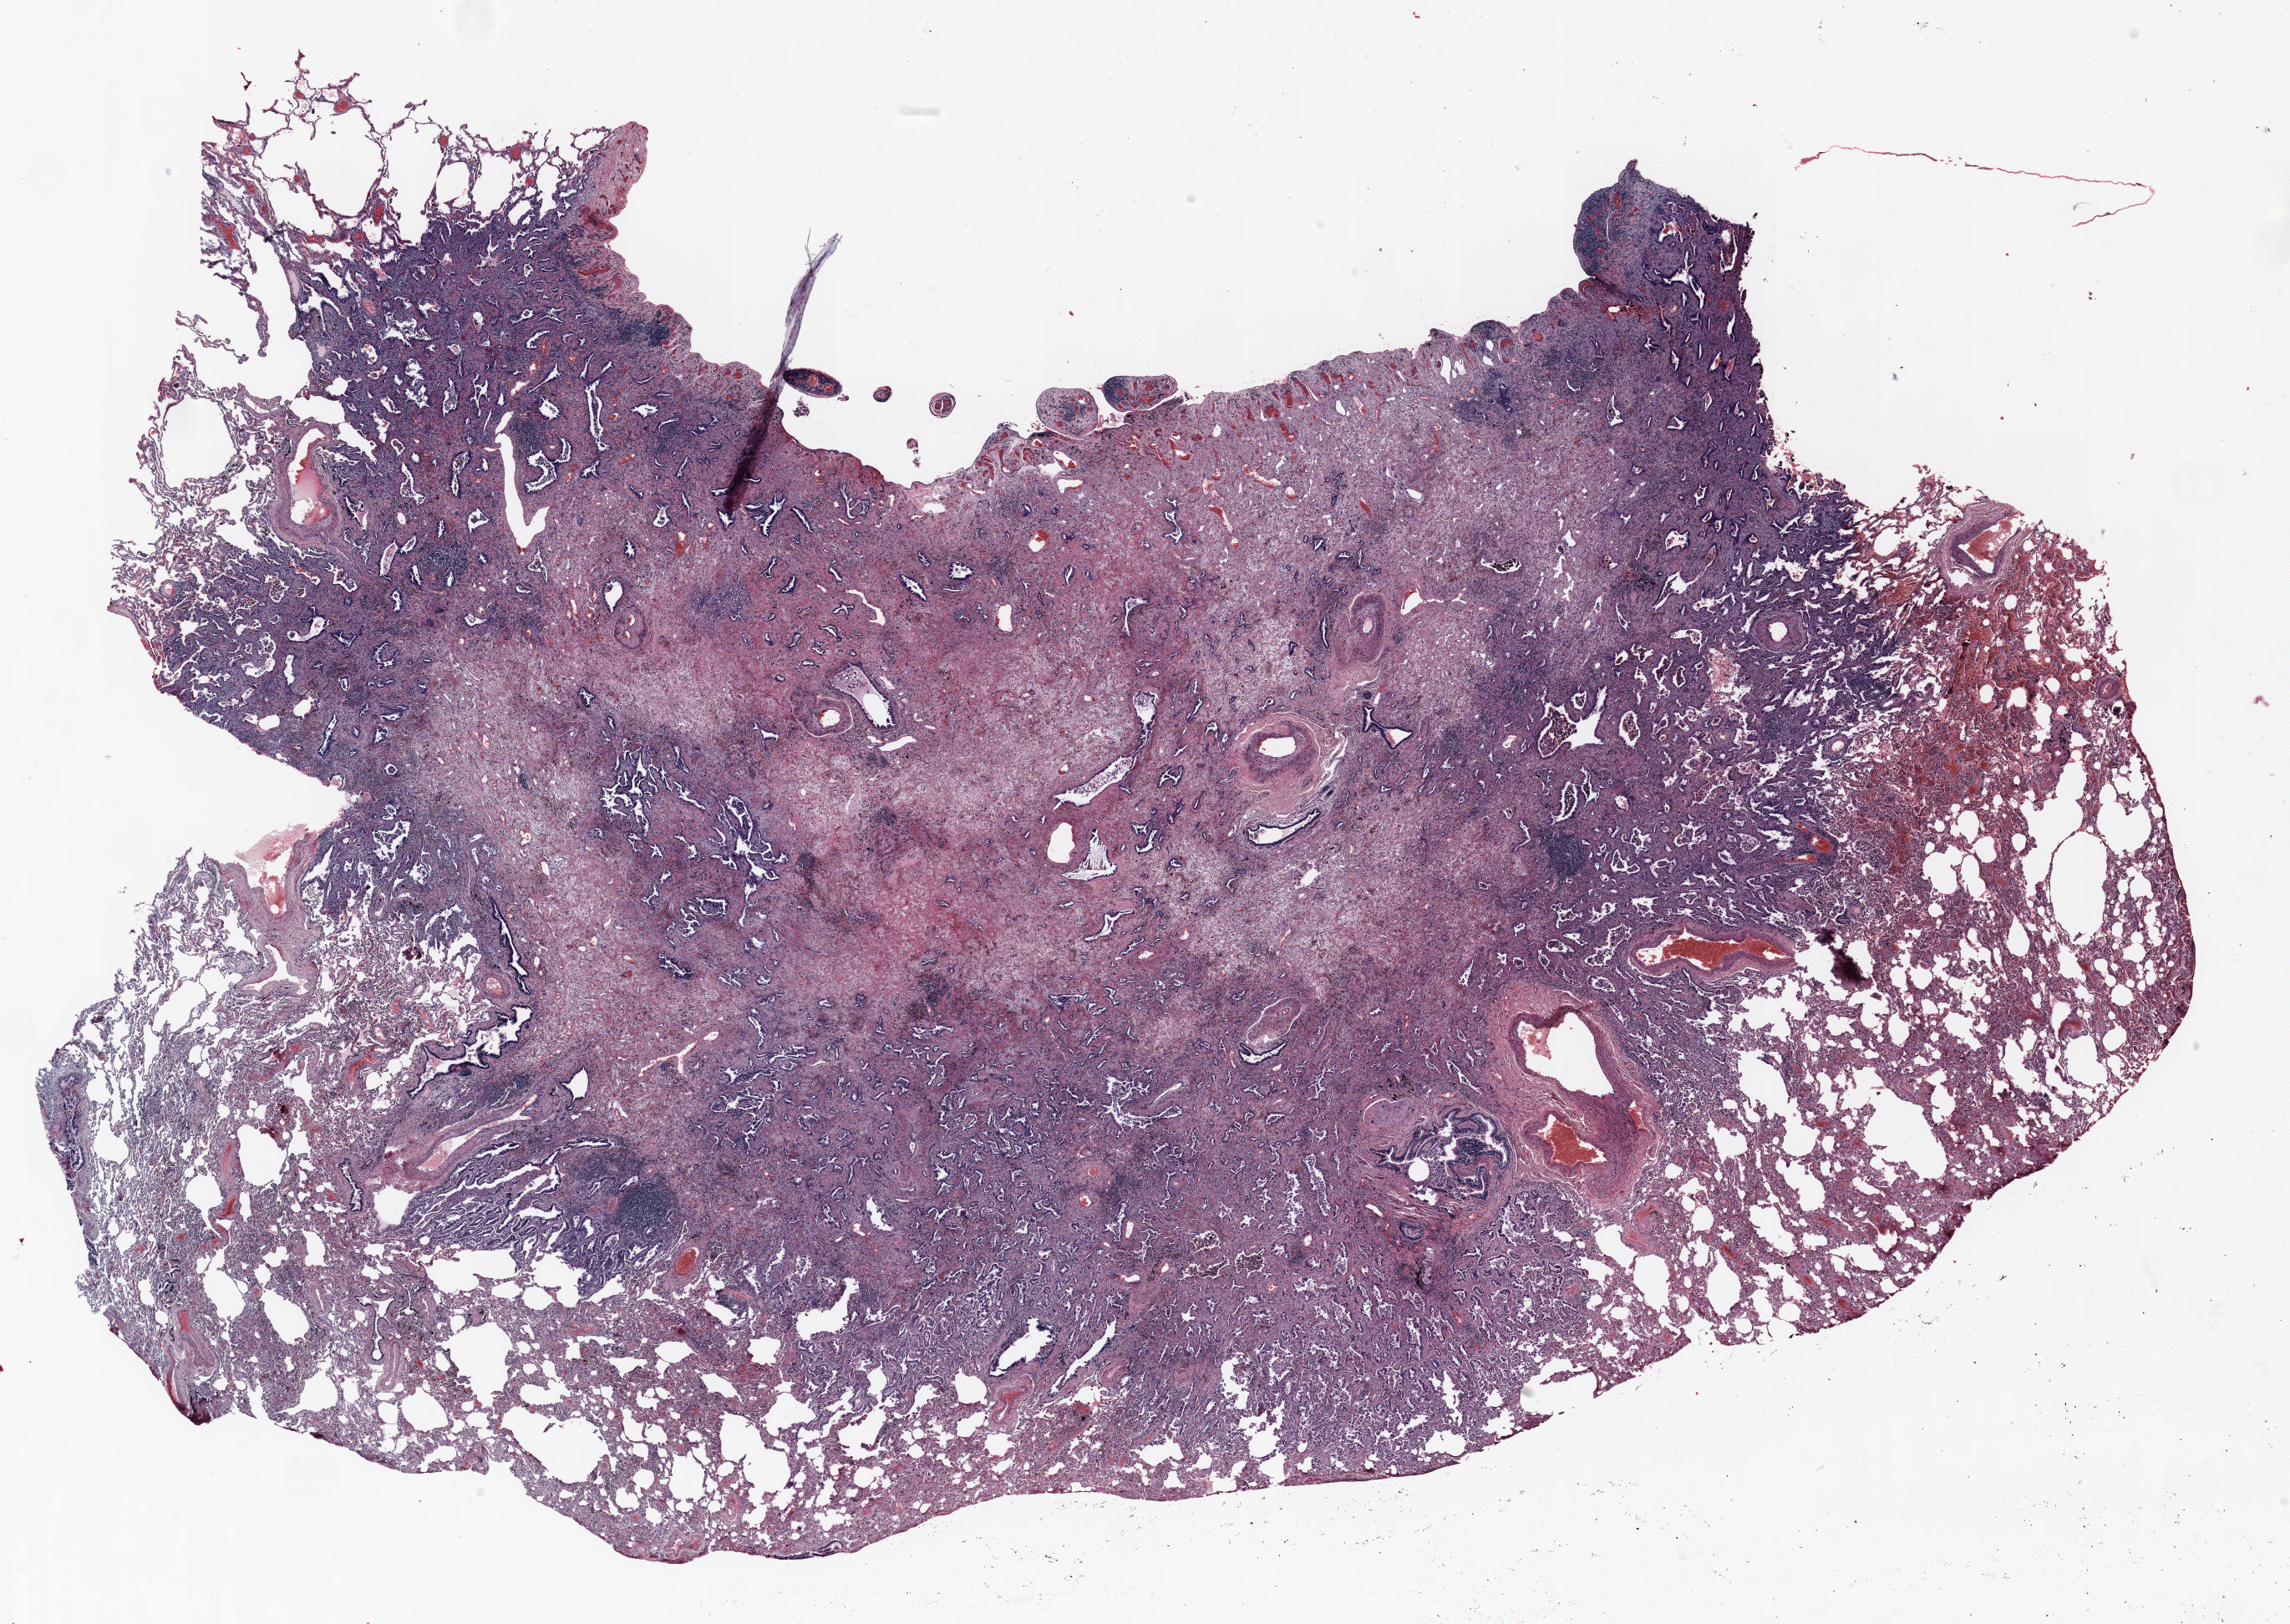
Hematoxylin and eosin (H&E) stained whole-slide image, shown as a low-resolution overview of the whole scanned area (about 22.0 x 15.6 mm, acquisition: 20x scan). Formalin-fixed paraffin-embedded (FFPE) section. Lung. Male patient, aged 62 at enrolment. Current smoker at enrolment.
Stage (AJCC 6th edition): IA. Participant's lung-cancer diagnosis: Bronchiolo-alveolar adenocarcinoma, NOS (ICD-O-3 8250/3). Primary tumour location (clinical record): left upper lobe. ICD-O-3 topography: upper lobe of lung (C34.1). Tumour size (pathology): 15 mm.